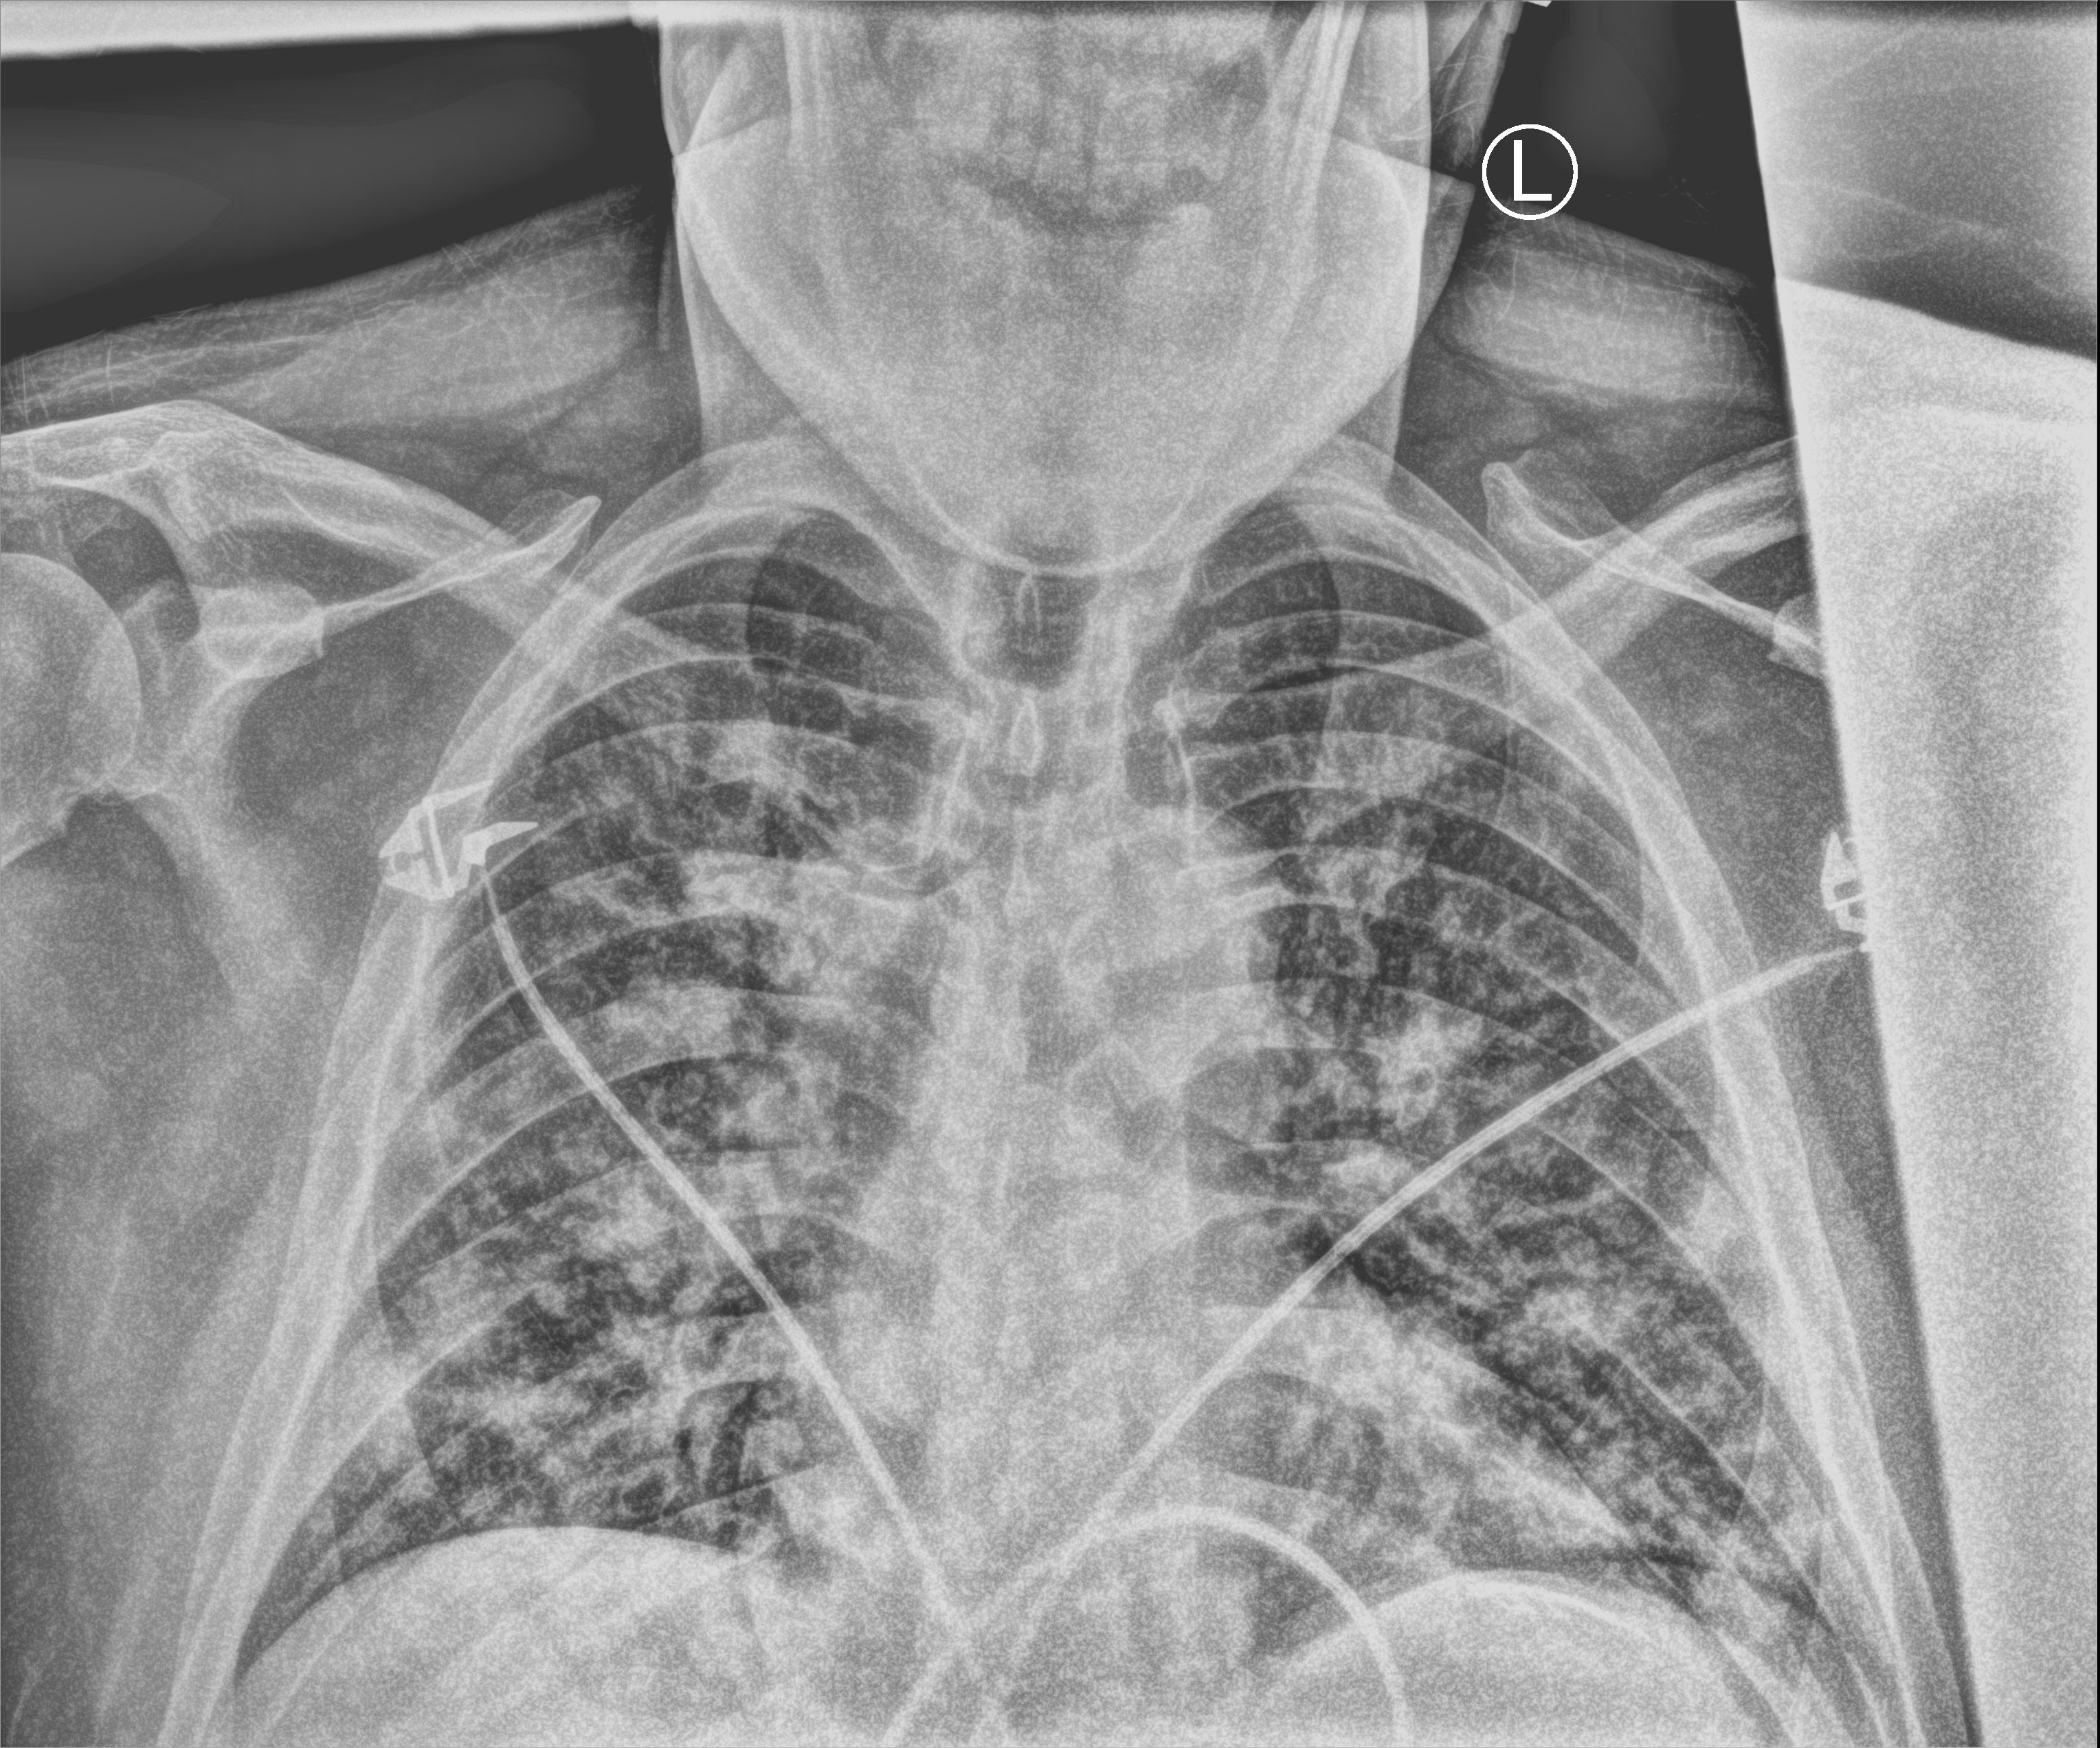
Portable chest radiograph, anteroposterior (AP) projection. Male patient hospitalised with COVID-19, age 18–59 years.
Admission-level facts for this patient (not findings on this image; timing relative to this image not recorded): mechanically ventilated during this hospital stay: no.